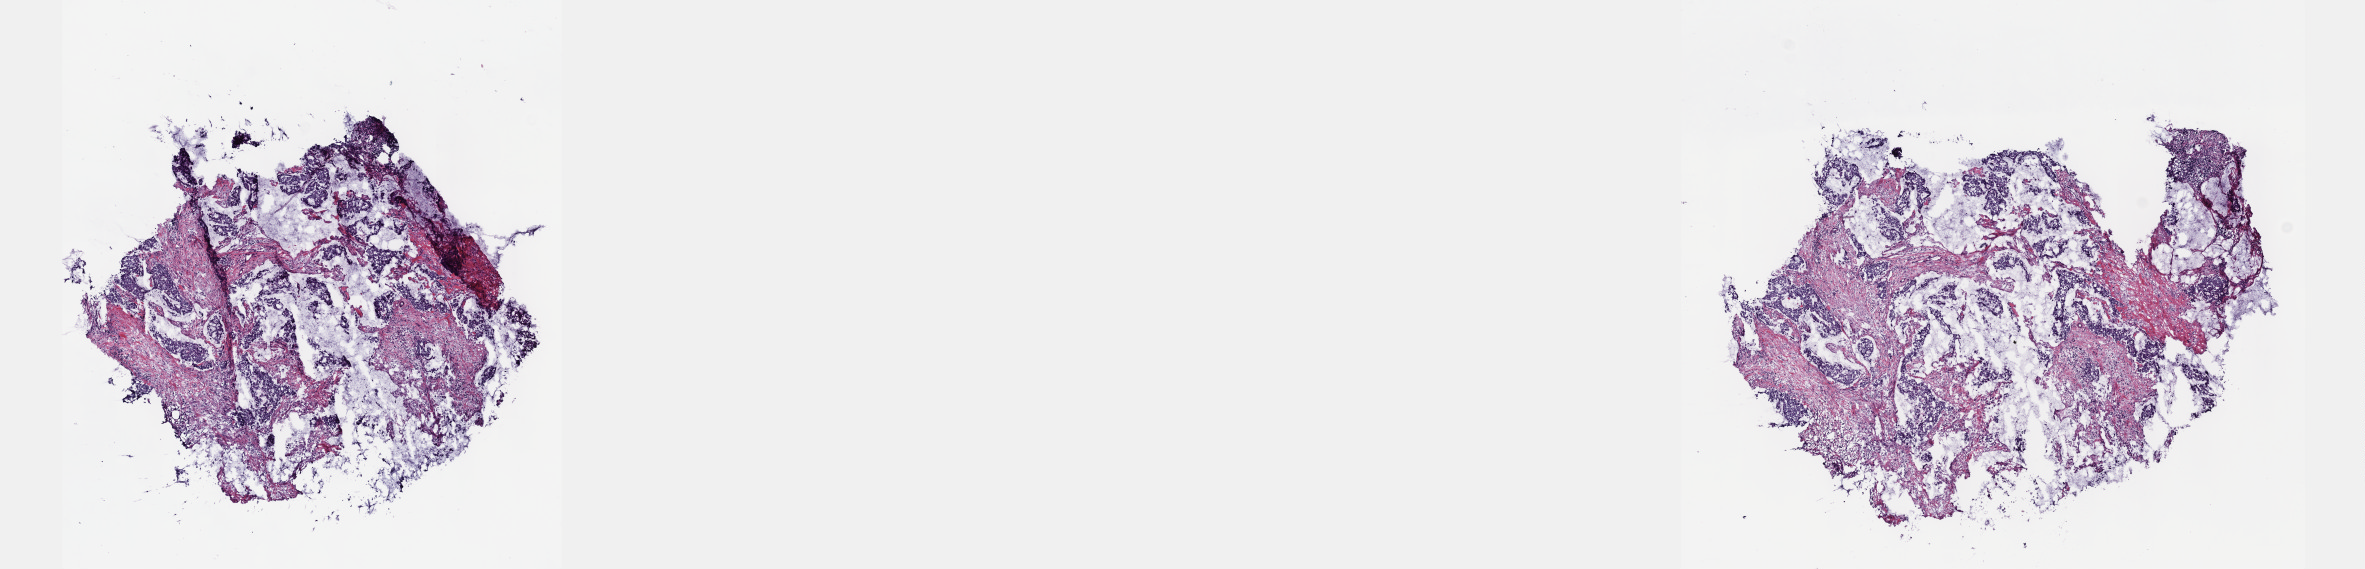
Digitized H&E-stained tissue section (whole slide), whole scanned area (about 19.1 x 4.6 mm, from a 40x scan) shown as a low-resolution overview, frozen section from the top of the tissue portion, sample: primary tumour, bile duct. Female patient.
Diagnosis: Cholangiocarcinoma (head of pancreas).